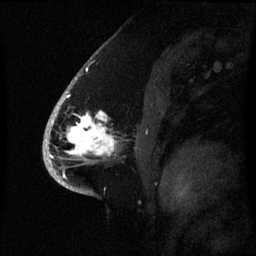
Breast MRI (dynamic contrast-enhanced), one sagittal slice; slice 43 of 60 in the series (ordered by position); dynamic contrast-enhanced series, image 2 of 3 at this slice position (ordered by acquisition); 1.5 T; TE 4.2 ms, TR 8.4 ms; 2.1 mm slice thickness; 256 × 256 image matrix. Female patient, age 53 years. From the clinical record (not read from this slice): setting: breast cancer imaged before/during neoadjuvant chemotherapy; receptor status: HR-positive, HER2-negative.
Outlined on this slice (semi-automatic segmentation, software-assisted and operator-edited):
- analysis volume of interest (the breast-tissue region the enhancement analysis was run in; not a lesion): bounding box (x1, y1, x2, y2) in pixels: (52, 90, 120, 171)
- tumour enhancement mask (voxels above the 70 % enhancement threshold inside the analysis volume of interest): (52, 98, 115, 157)